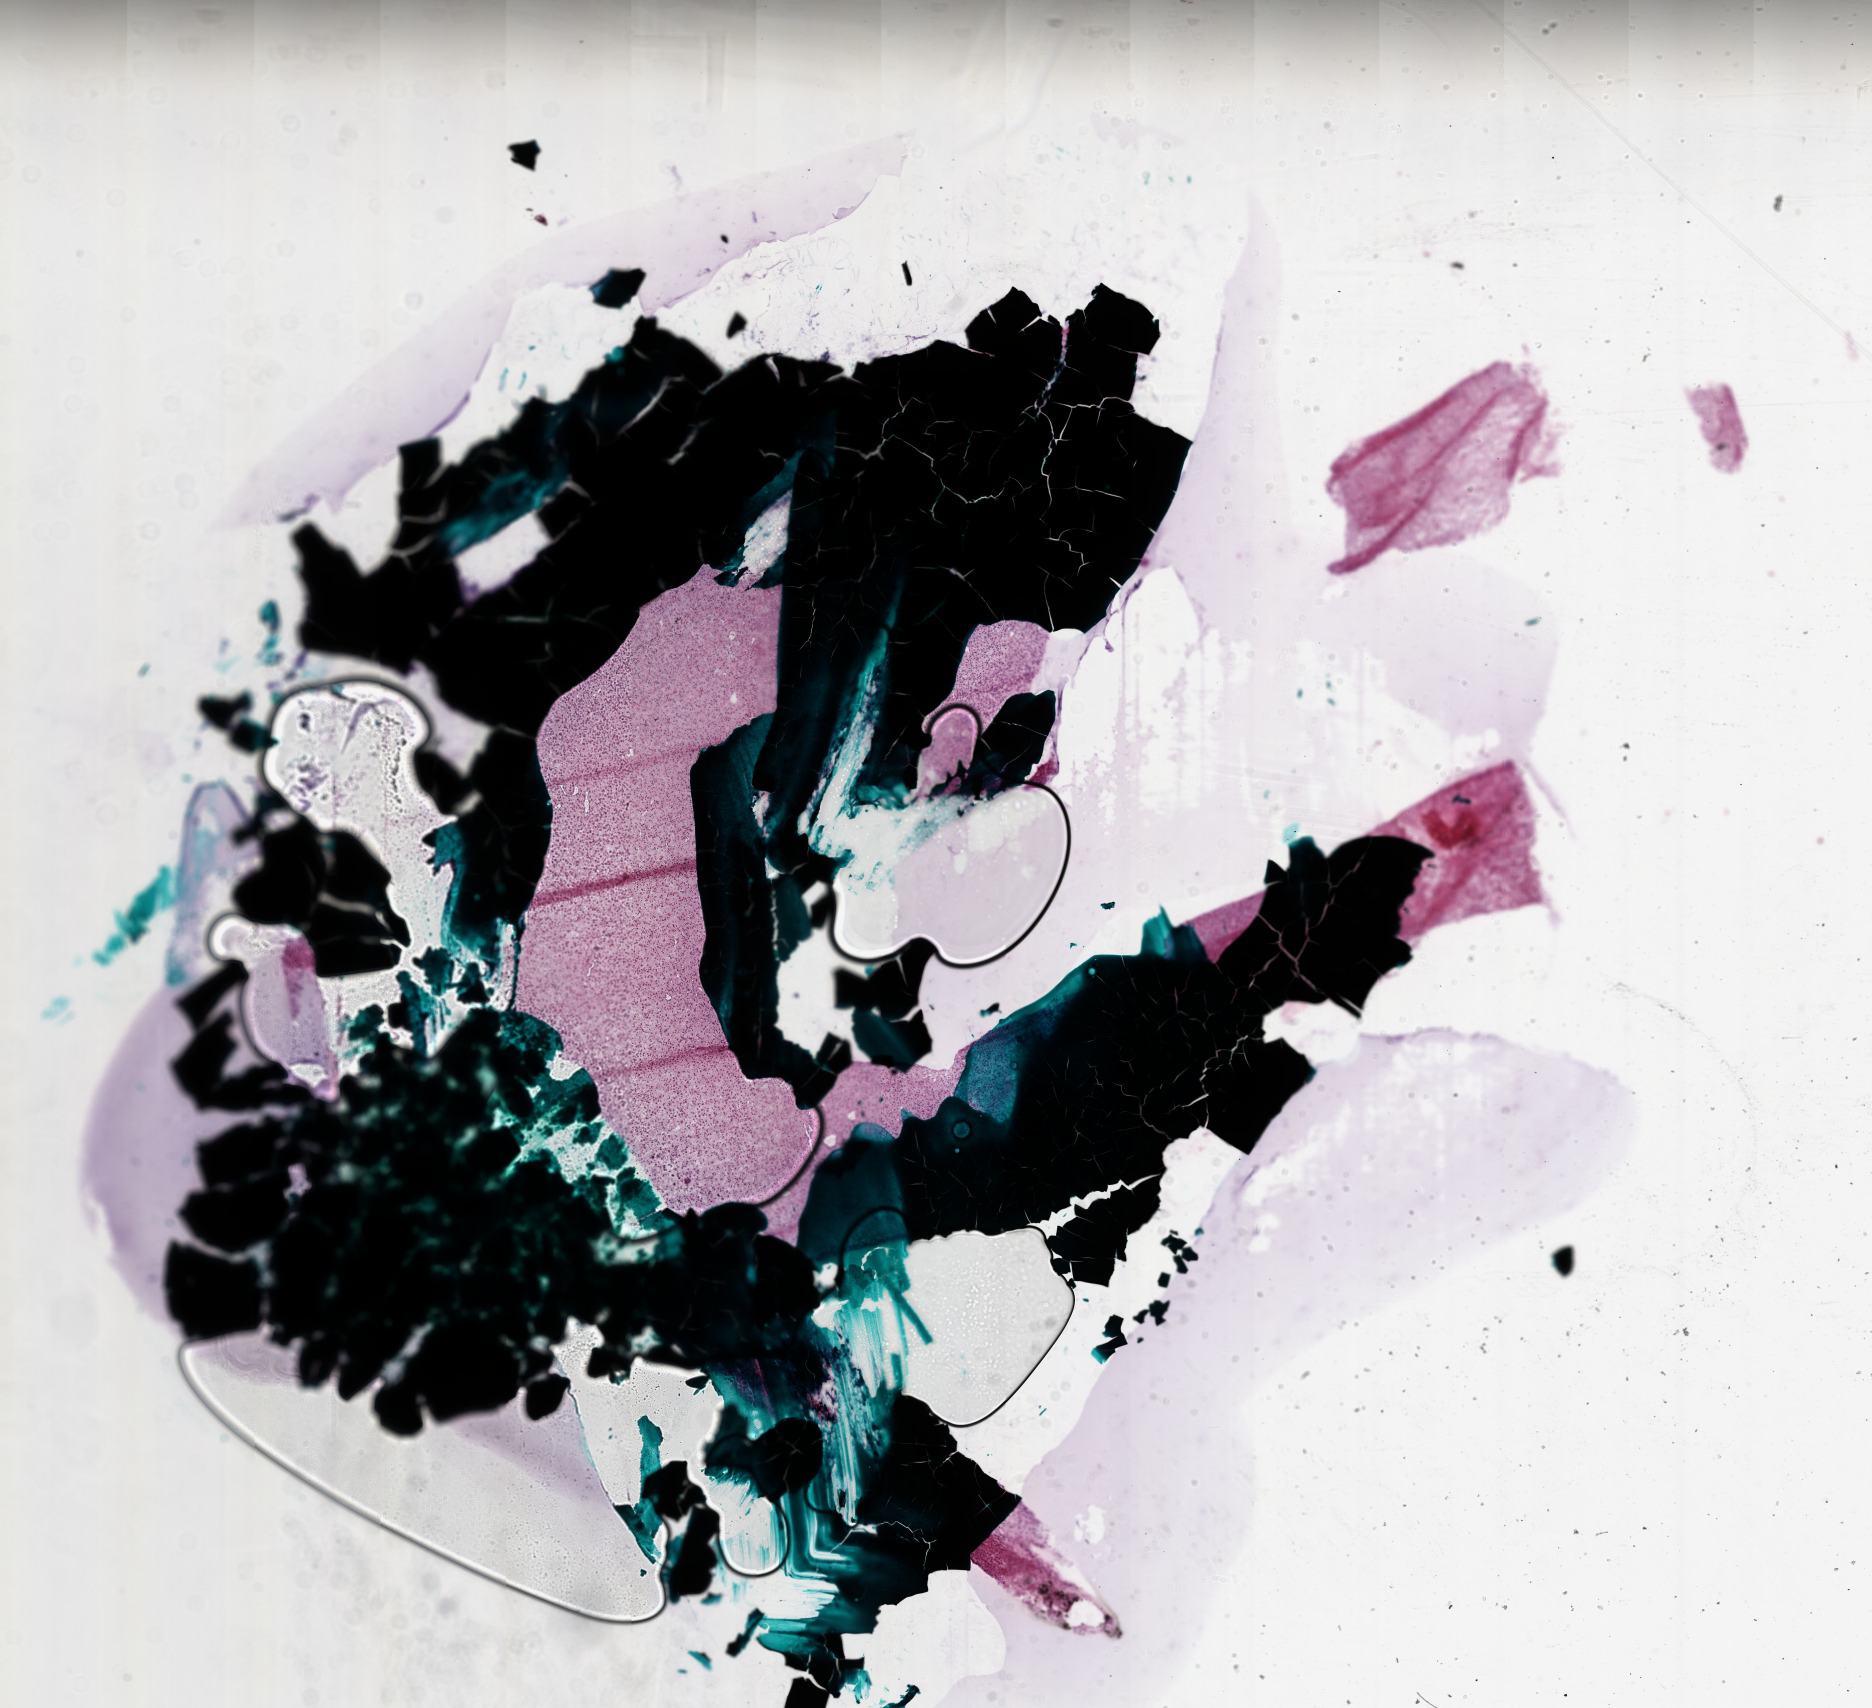
Whole-slide histology image, H&E-stained, whole scanned area (about 15.0 x 13.7 mm) shown as a low-resolution overview, frozen section, primary tumour sample from the brain. Male patient; age at initial diagnosis 43 years. Composition of this section per pathologist review: tumour cells 100%, tumour nuclei 100%, normal cells 0%, stromal cells 0%, necrosis 0%. Inflammatory infiltration, as recorded: lymphocyte infiltration 0%, monocyte infiltration 0%, neutrophil infiltration 0%.
• histologic diagnosis: Glioblastoma